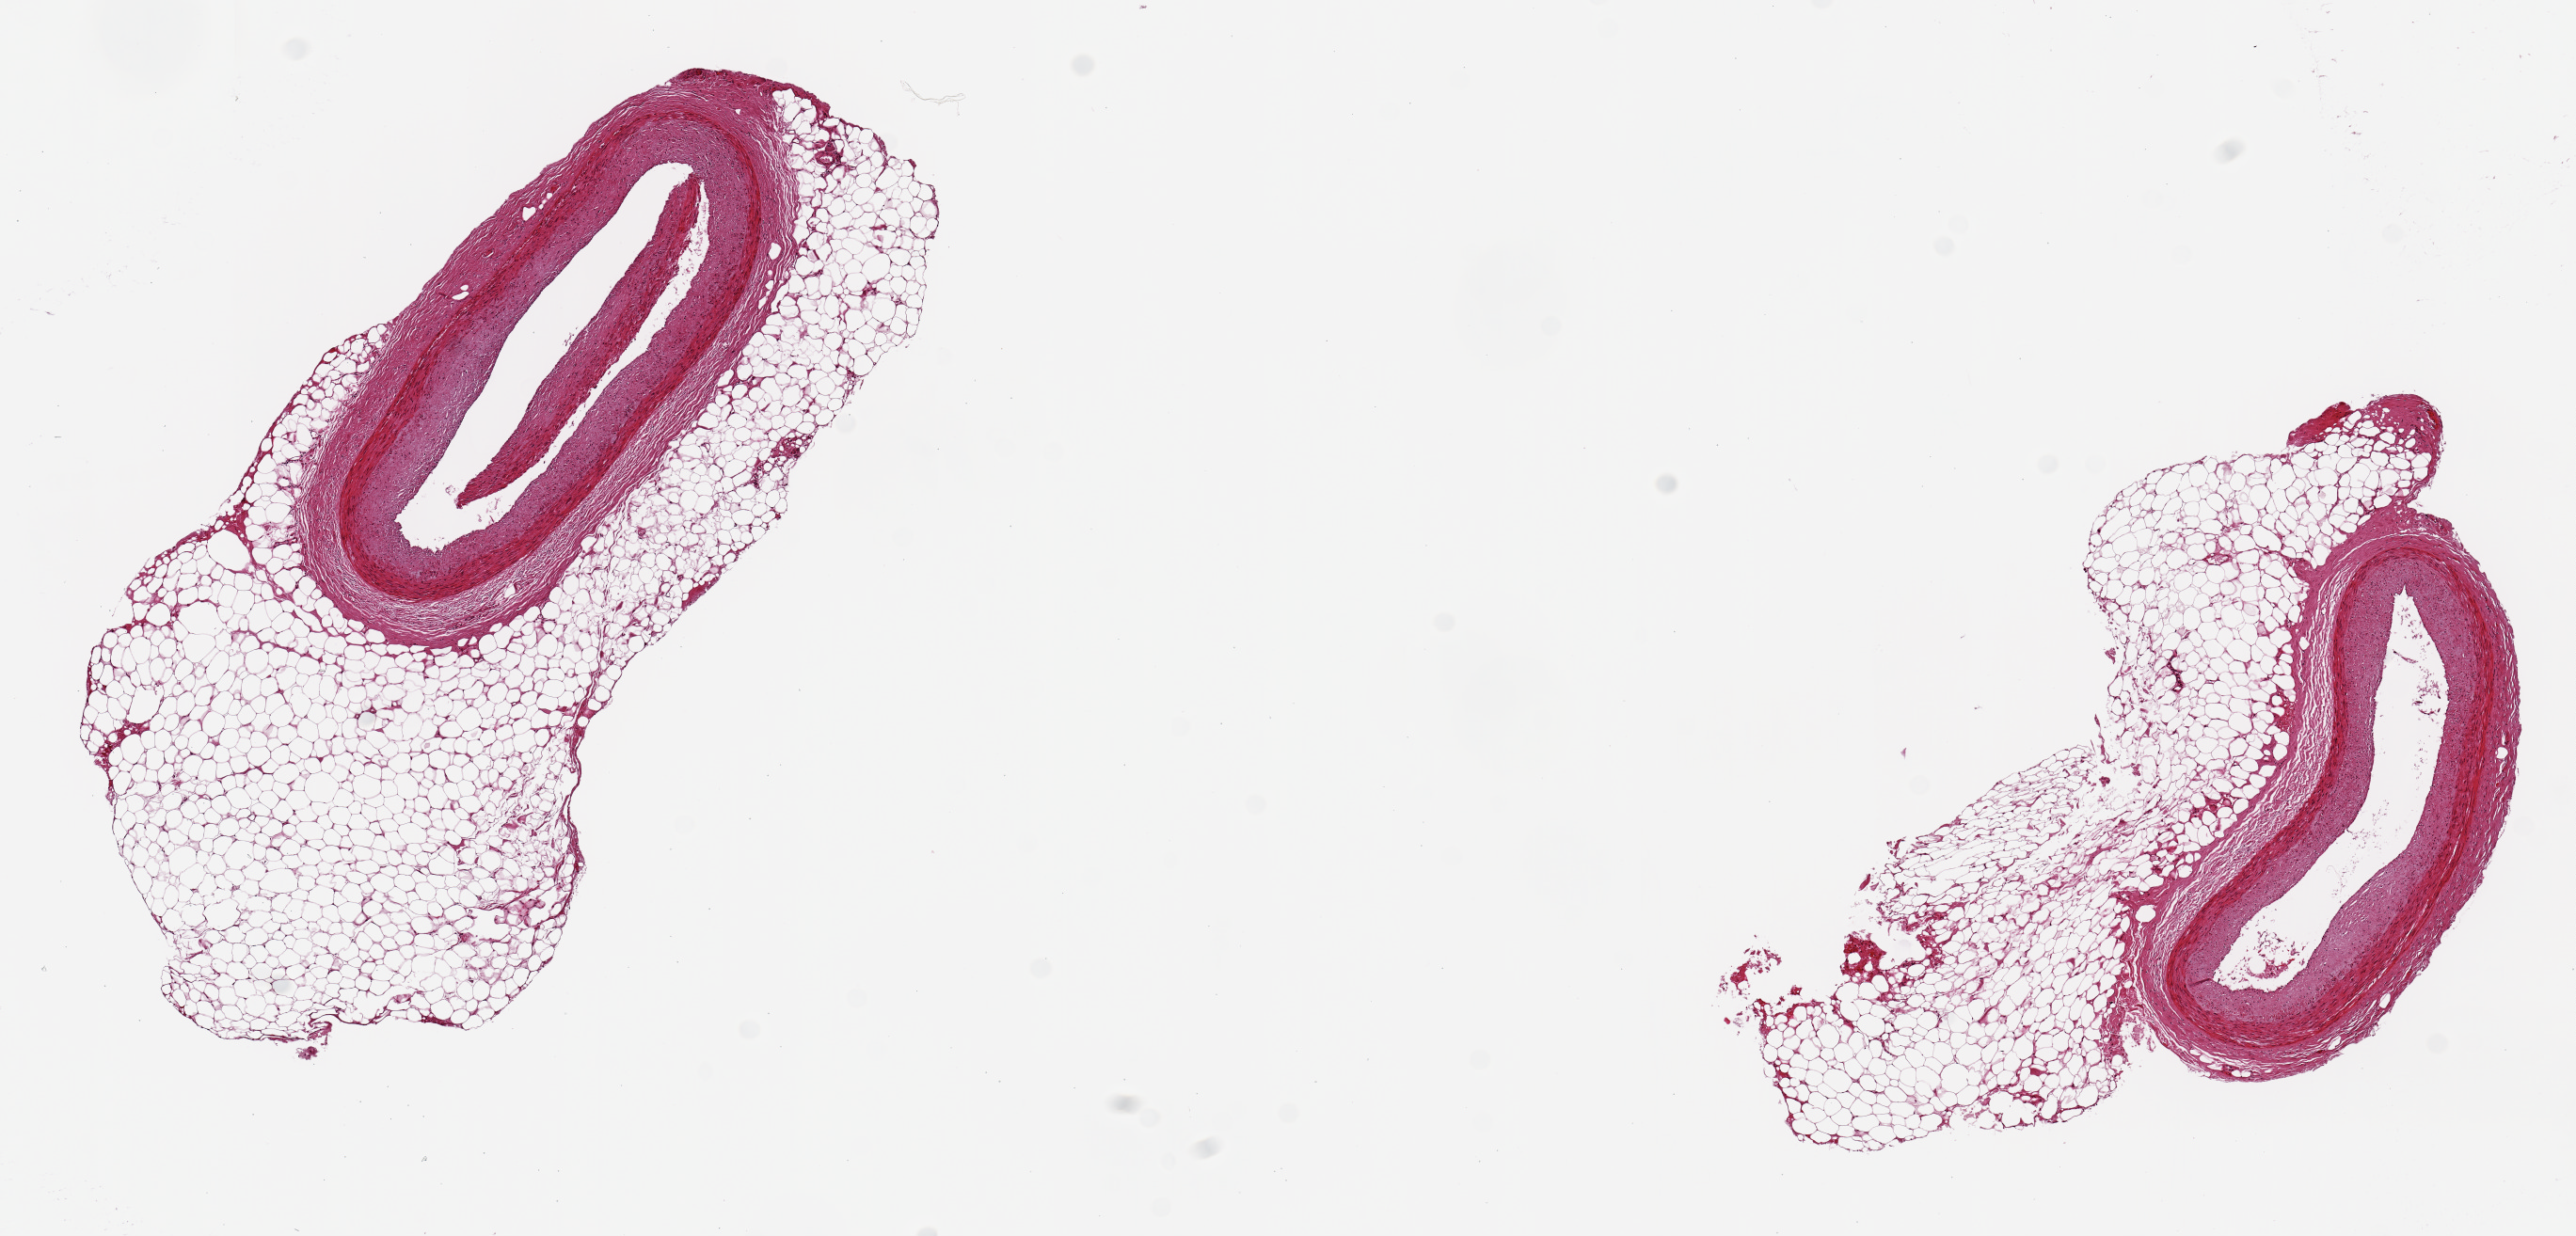
Hematoxylin and eosin (H&E) whole-slide image, brightfield, whole scanned area (about 10.8 x 5.2 mm, acquisition: 20x scan) shown as a low-resolution overview. Donor: male.
* specimen: PAXgene-fixed, paraffin-embedded tissue; section of coronary artery (target tissue); donor tissue sample